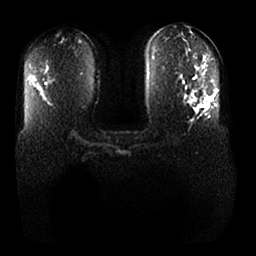
Breast MRI, one axial slice. Slice 18 of 25 in the series (ordered by position). Diffusion-weighted series; image 2 of 4 stored at this slice position (different b-values; order by instance number). 1.5 T. 4 mm slice thickness. 256 × 256 image matrix, field of view 370 × 370 mm. Female patient.
Structures marked on this image (manually delineated by an expert):
- tumour on diffusion-weighted imaging: bounding box [x1, y1, x2, y2] px = [187, 94, 210, 105]